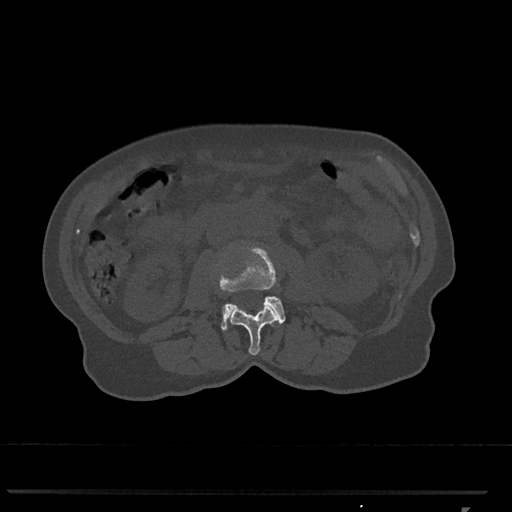
CT including the spine, one axial slice. Position 304 of 793 along the scan axis. Reconstruction kernel Br40s/3. 120 kVp. Bone window (W 1800 / L 400 HU). 0.5 mm slice thickness. 512 × 512 image matrix. Female patient, age 62 years. From the clinical record (not read from this slice): primary cancer: renal.
Annotated regions visible in this slice (semi-automatic segmentation, software-assisted and operator-edited):
- L2 vertebra: box from (x=229, y=304) to (x=278, y=355) px
- L3 vertebra: (x=219, y=247)–(x=285, y=331)